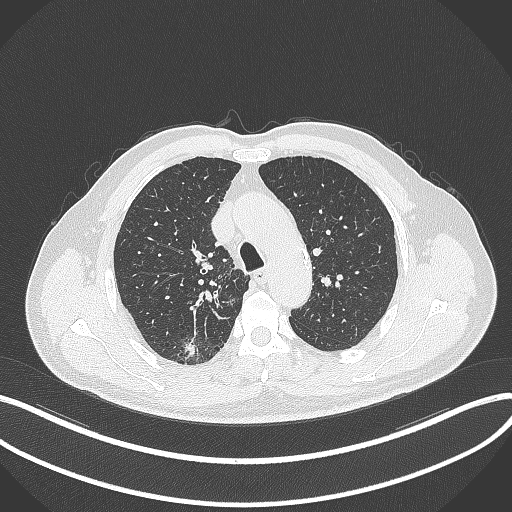
Chest CT, one axial slice; slice 274 of 359 in the series (ordered by position); reconstruction kernel B70f; 120 kVp; lung window (W 1500 / L -600 HU); 1 mm slice thickness; 512 × 512 image matrix, field of view 400 × 400 mm. Male patient, age 69 years. Case-level facts recorded for this patient, not image findings: clinical TNM (as recorded): T1b N0 M0.
Outlined on this slice (bounding box drawn by a radiologist):
- lung tumour (recorded histology: adenocarcinoma): bounding box (x1, y1, x2, y2) in pixels: (176, 336, 201, 364)